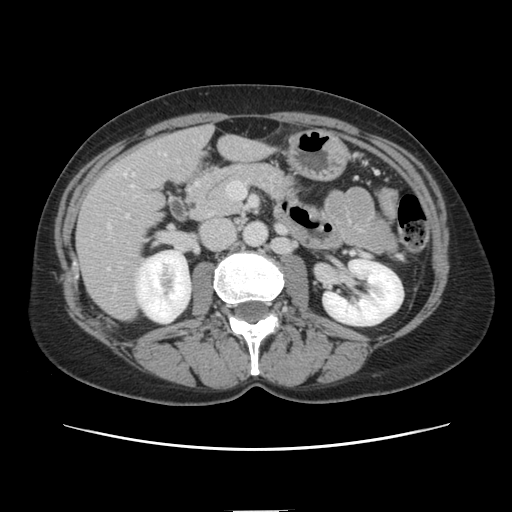
Contrast-enhanced abdominal CT, one axial slice; 120 kVp; intravenous contrast given; soft-tissue window (W 400 / L 40 HU); 2.5 mm slice thickness; 512 × 512 image matrix. Female patient, age 63 years. Case-level facts recorded for this patient, not image findings: diagnosis: colorectal cancer liver metastases, imaged before liver resection; multiple liver metastases: yes; largest metastasis: 3.2 cm; disease in both lobes: yes.
Annotated regions visible in this slice (expert manual segmentation):
- liver: bounding box [x1, y1, x2, y2] px = [77, 127, 267, 320]
- planned liver remnant (the part of the liver to remain after resection): [178, 128, 268, 174]
- portal vein (with intrahepatic branches): [109, 173, 126, 227]